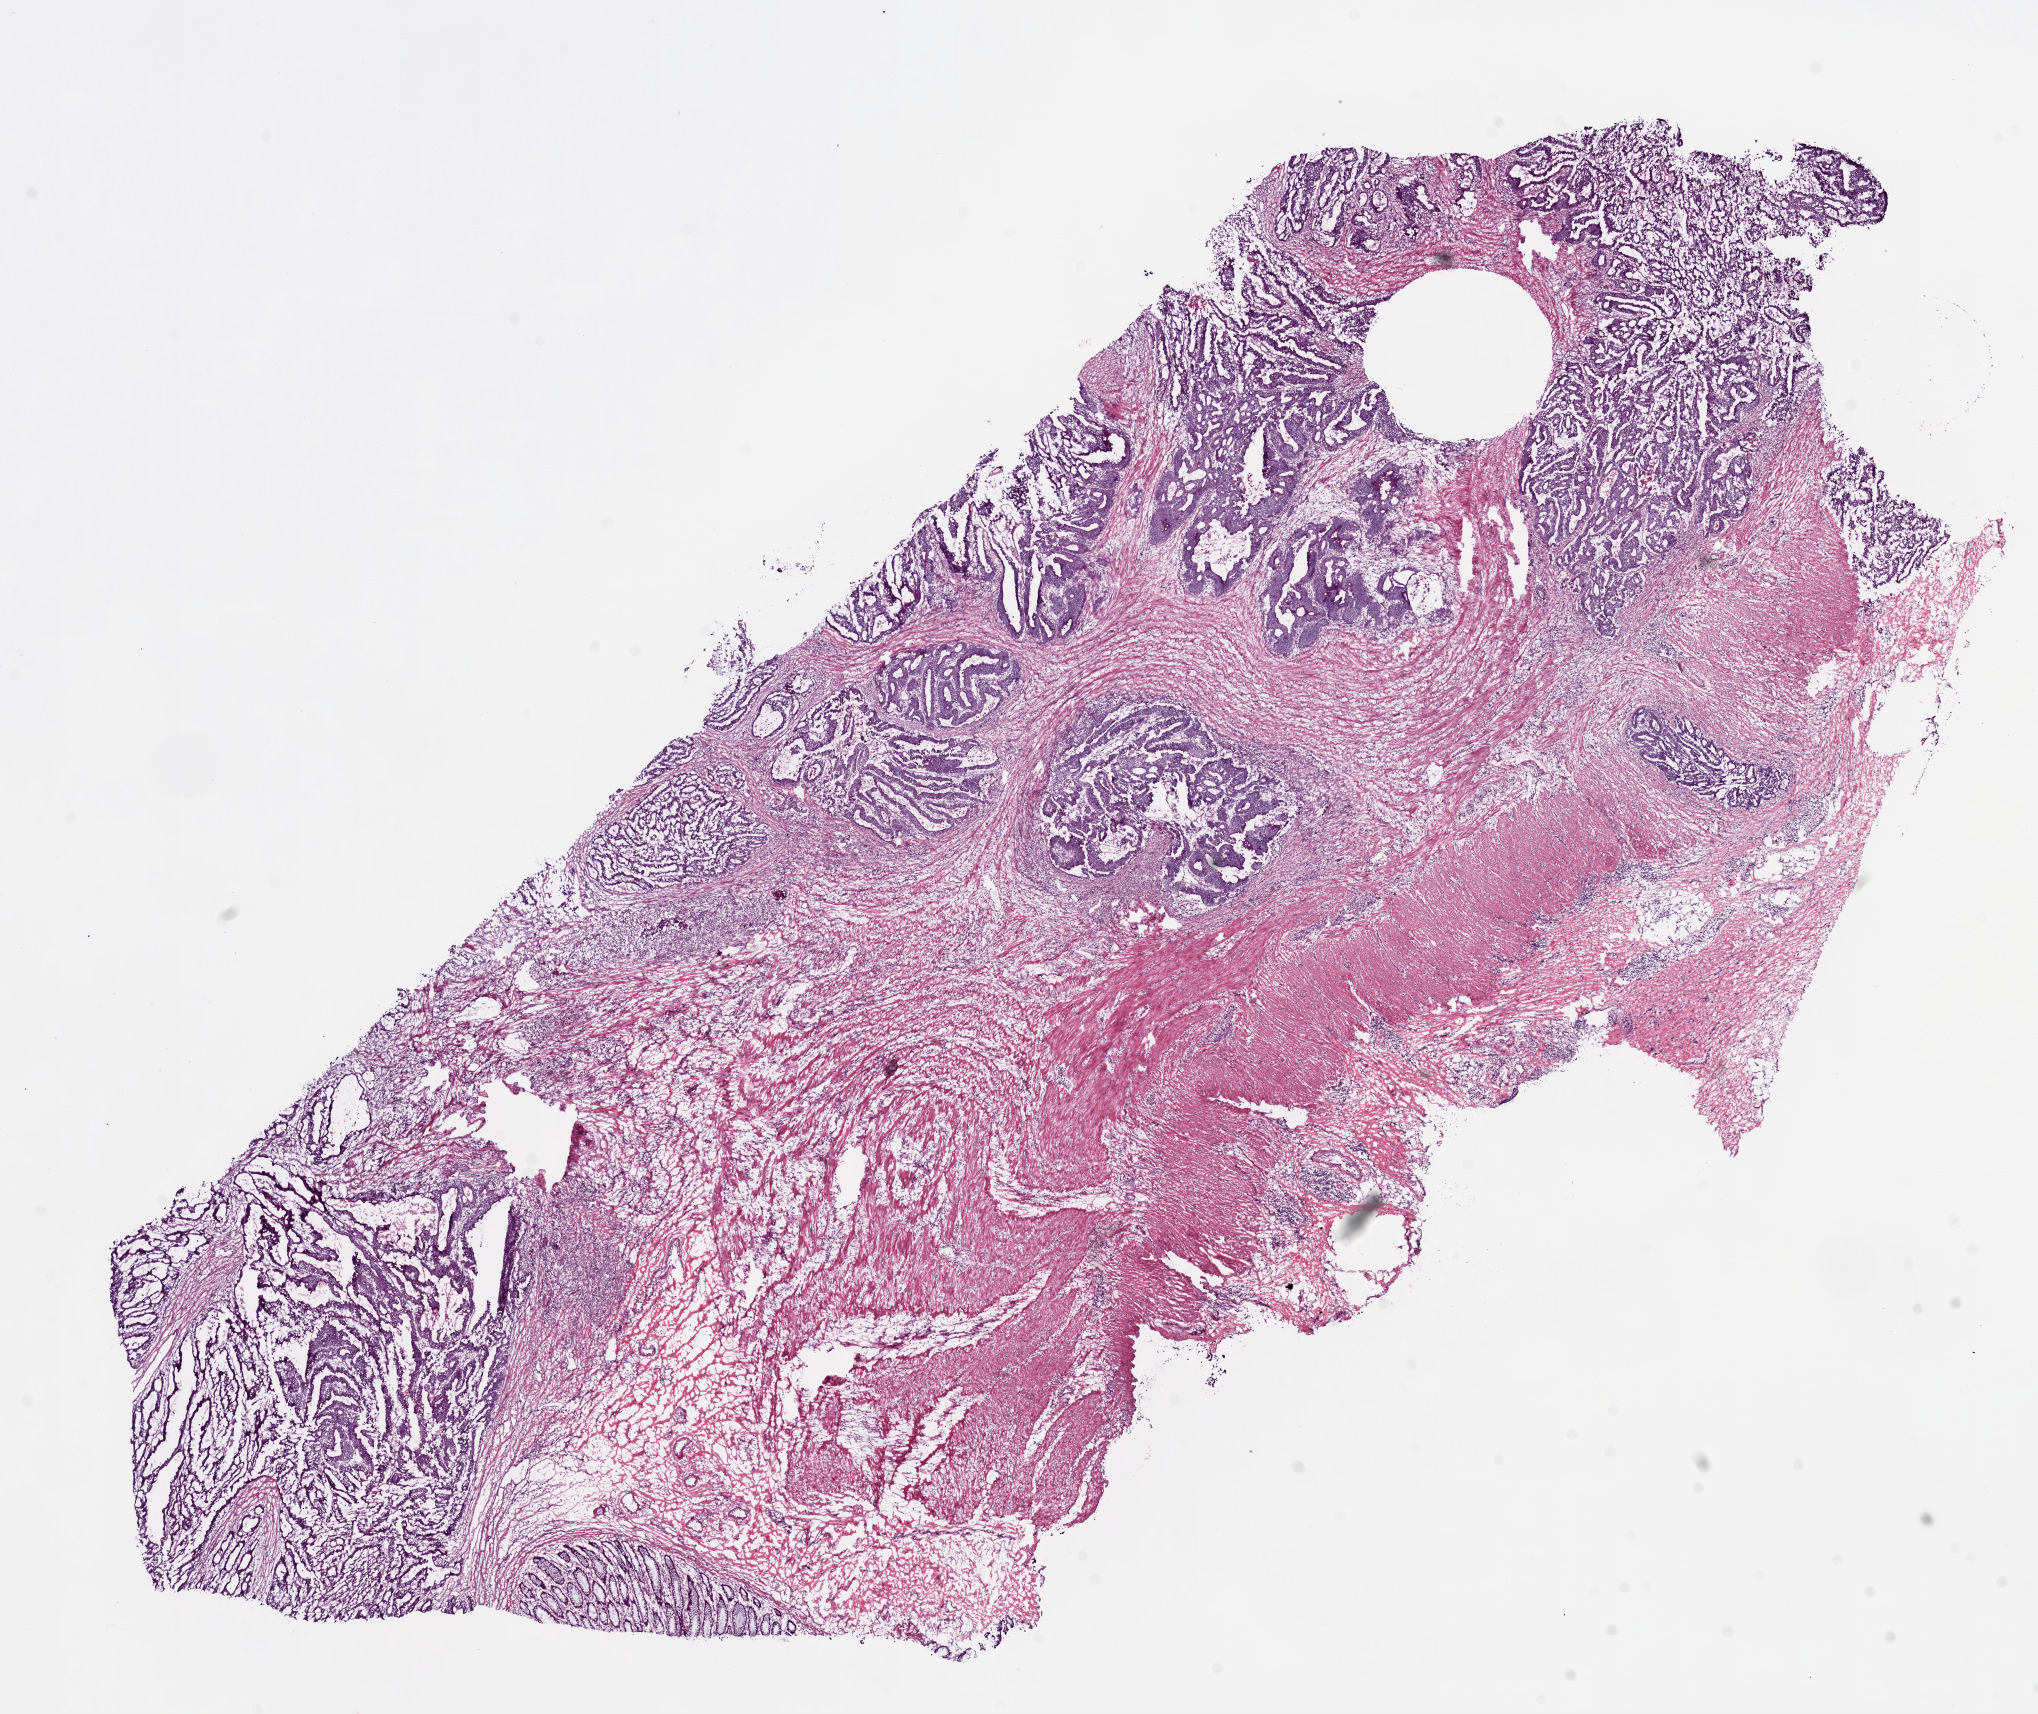
Digitized H&E tissue section (whole slide) — low-resolution overview of the scanned area, about 16.4 x 13.8 mm (from a 20x scan); frozen section from the bottom of the tissue portion; primary tumour sample from the colon. Patient: male, age at initial diagnosis 56 years. Composition of this section per pathologist review: tumour cells 69%, tumour nuclei 80%, normal cells 1%, stromal cells 30%, necrosis 0%.
Diagnosis: Adenocarcinoma, NOS. AJCC pathologic stage: IIA.